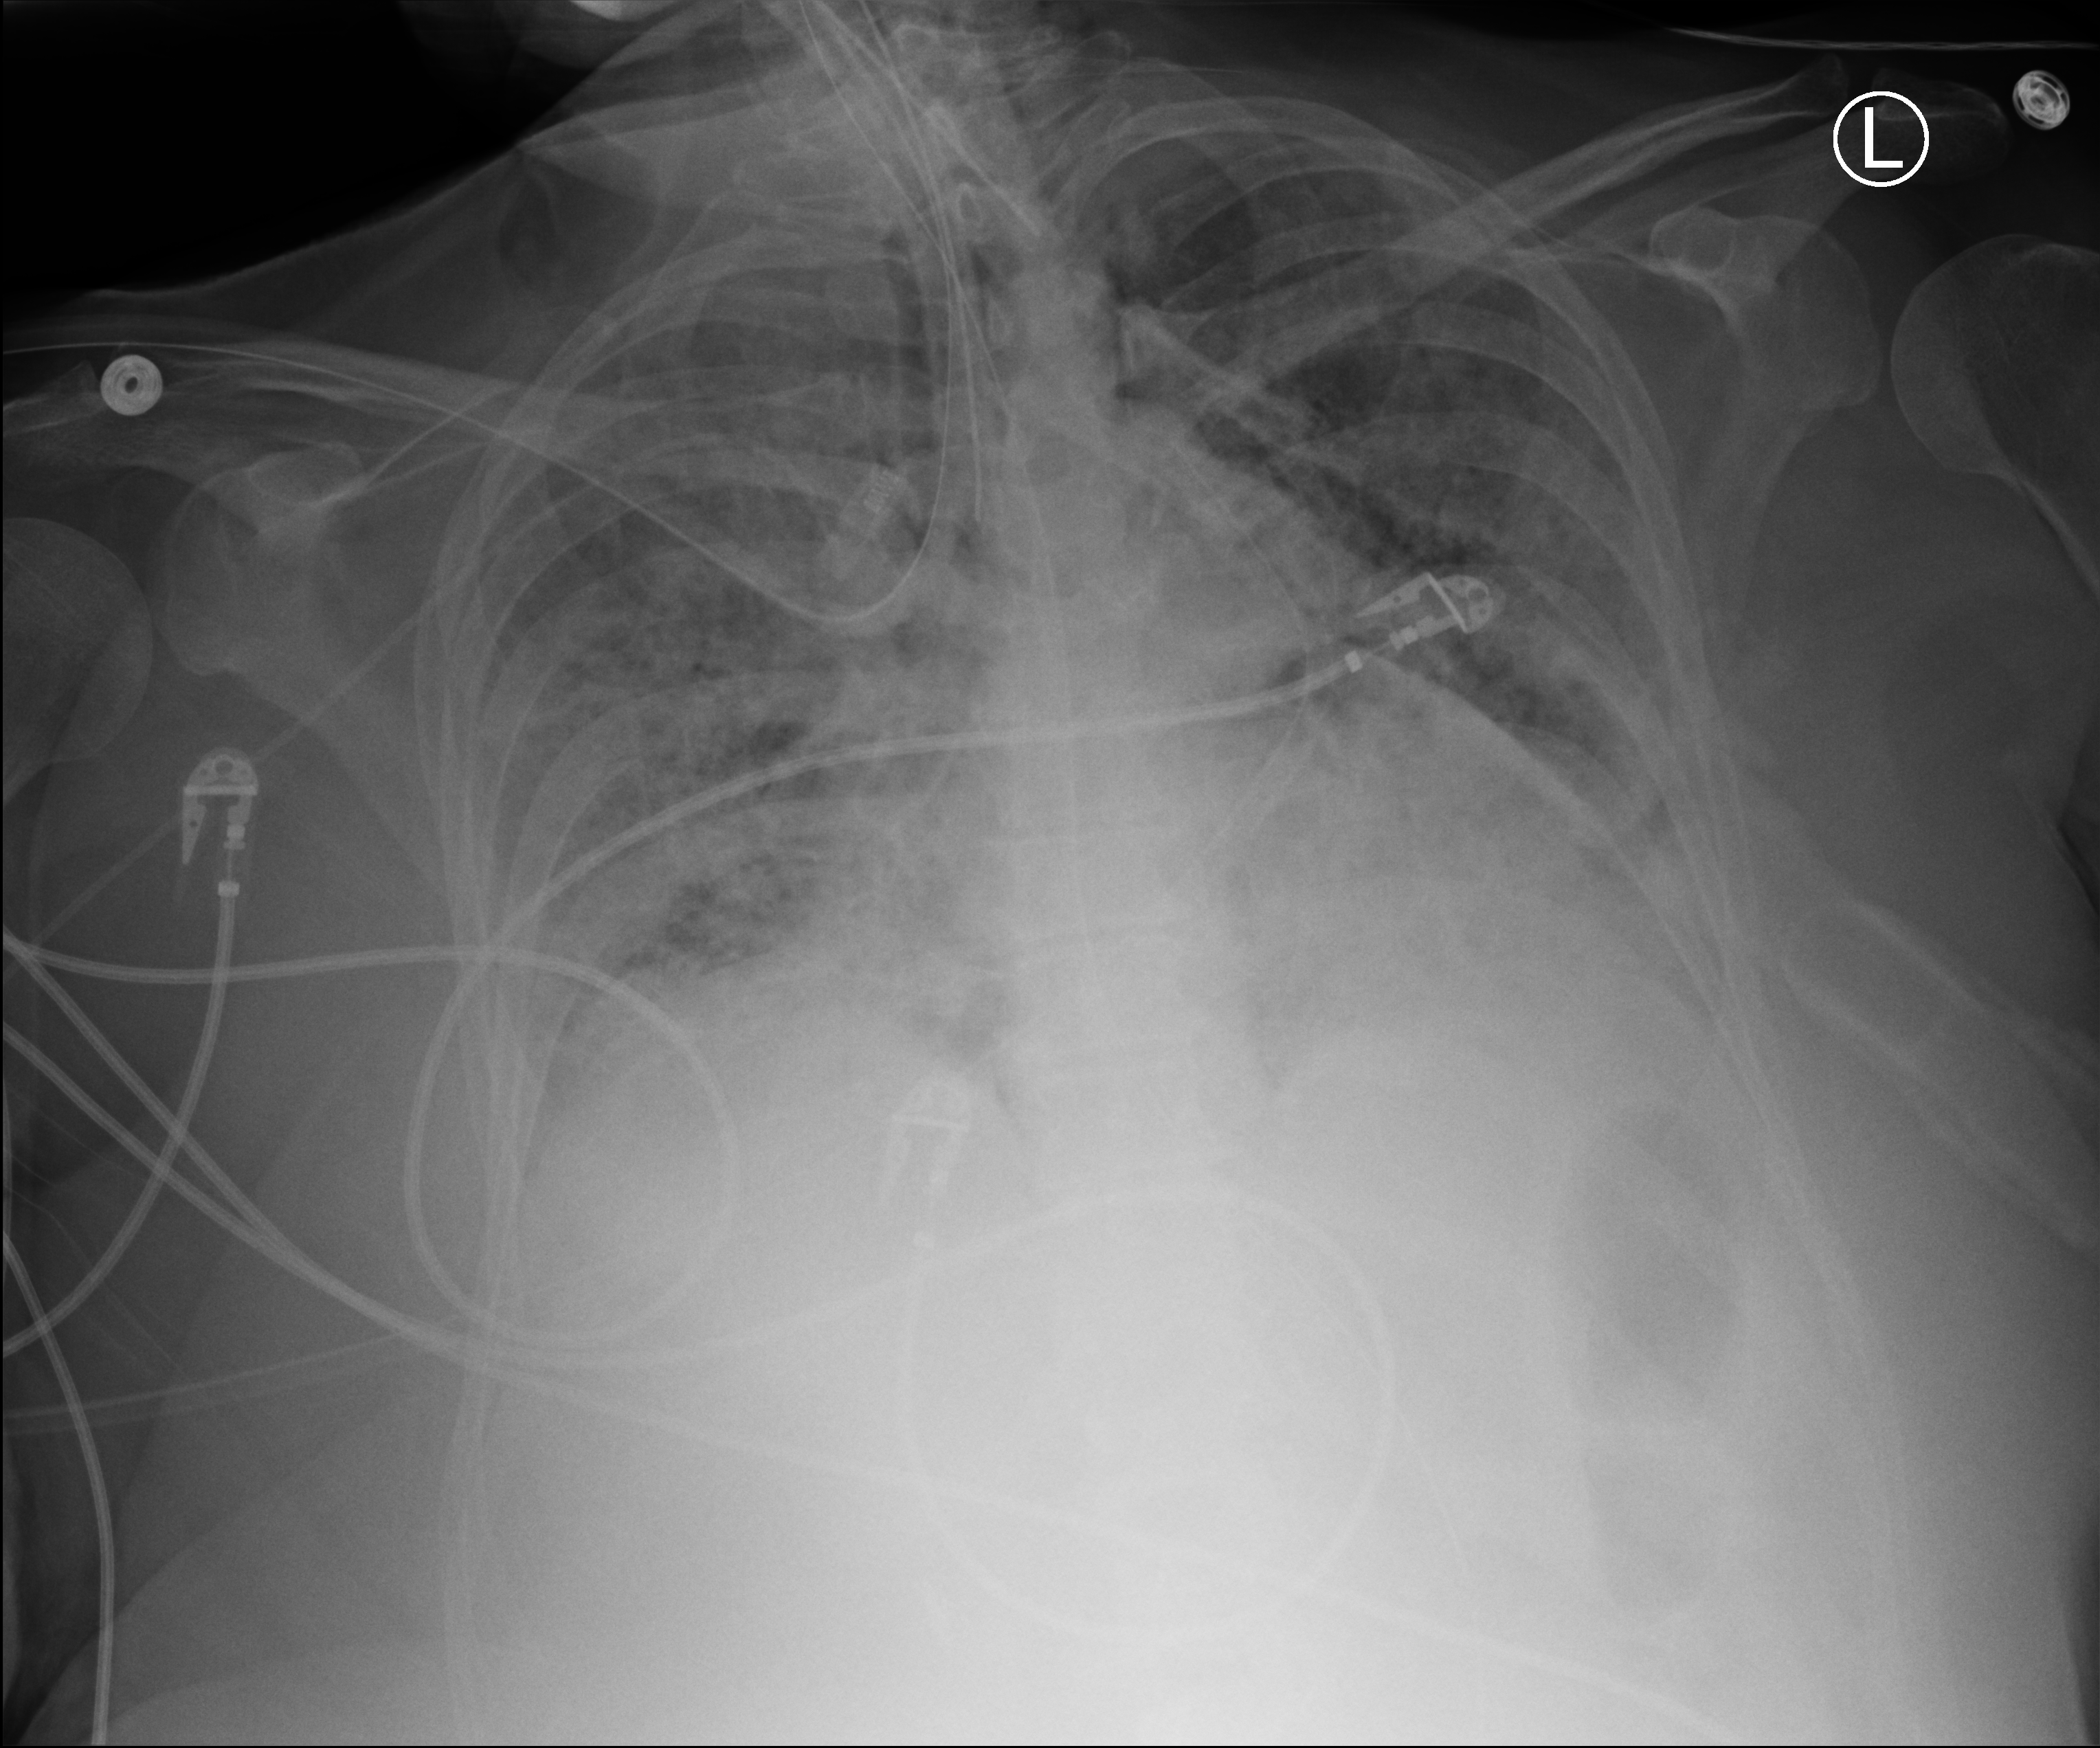
Portable chest radiograph. Female patient hospitalised with COVID-19, age 60–74 years.
Hospital-stay facts (about this admission, not read from this image; timing relative to this image not recorded):
- mechanically ventilated during this hospital stay: yes